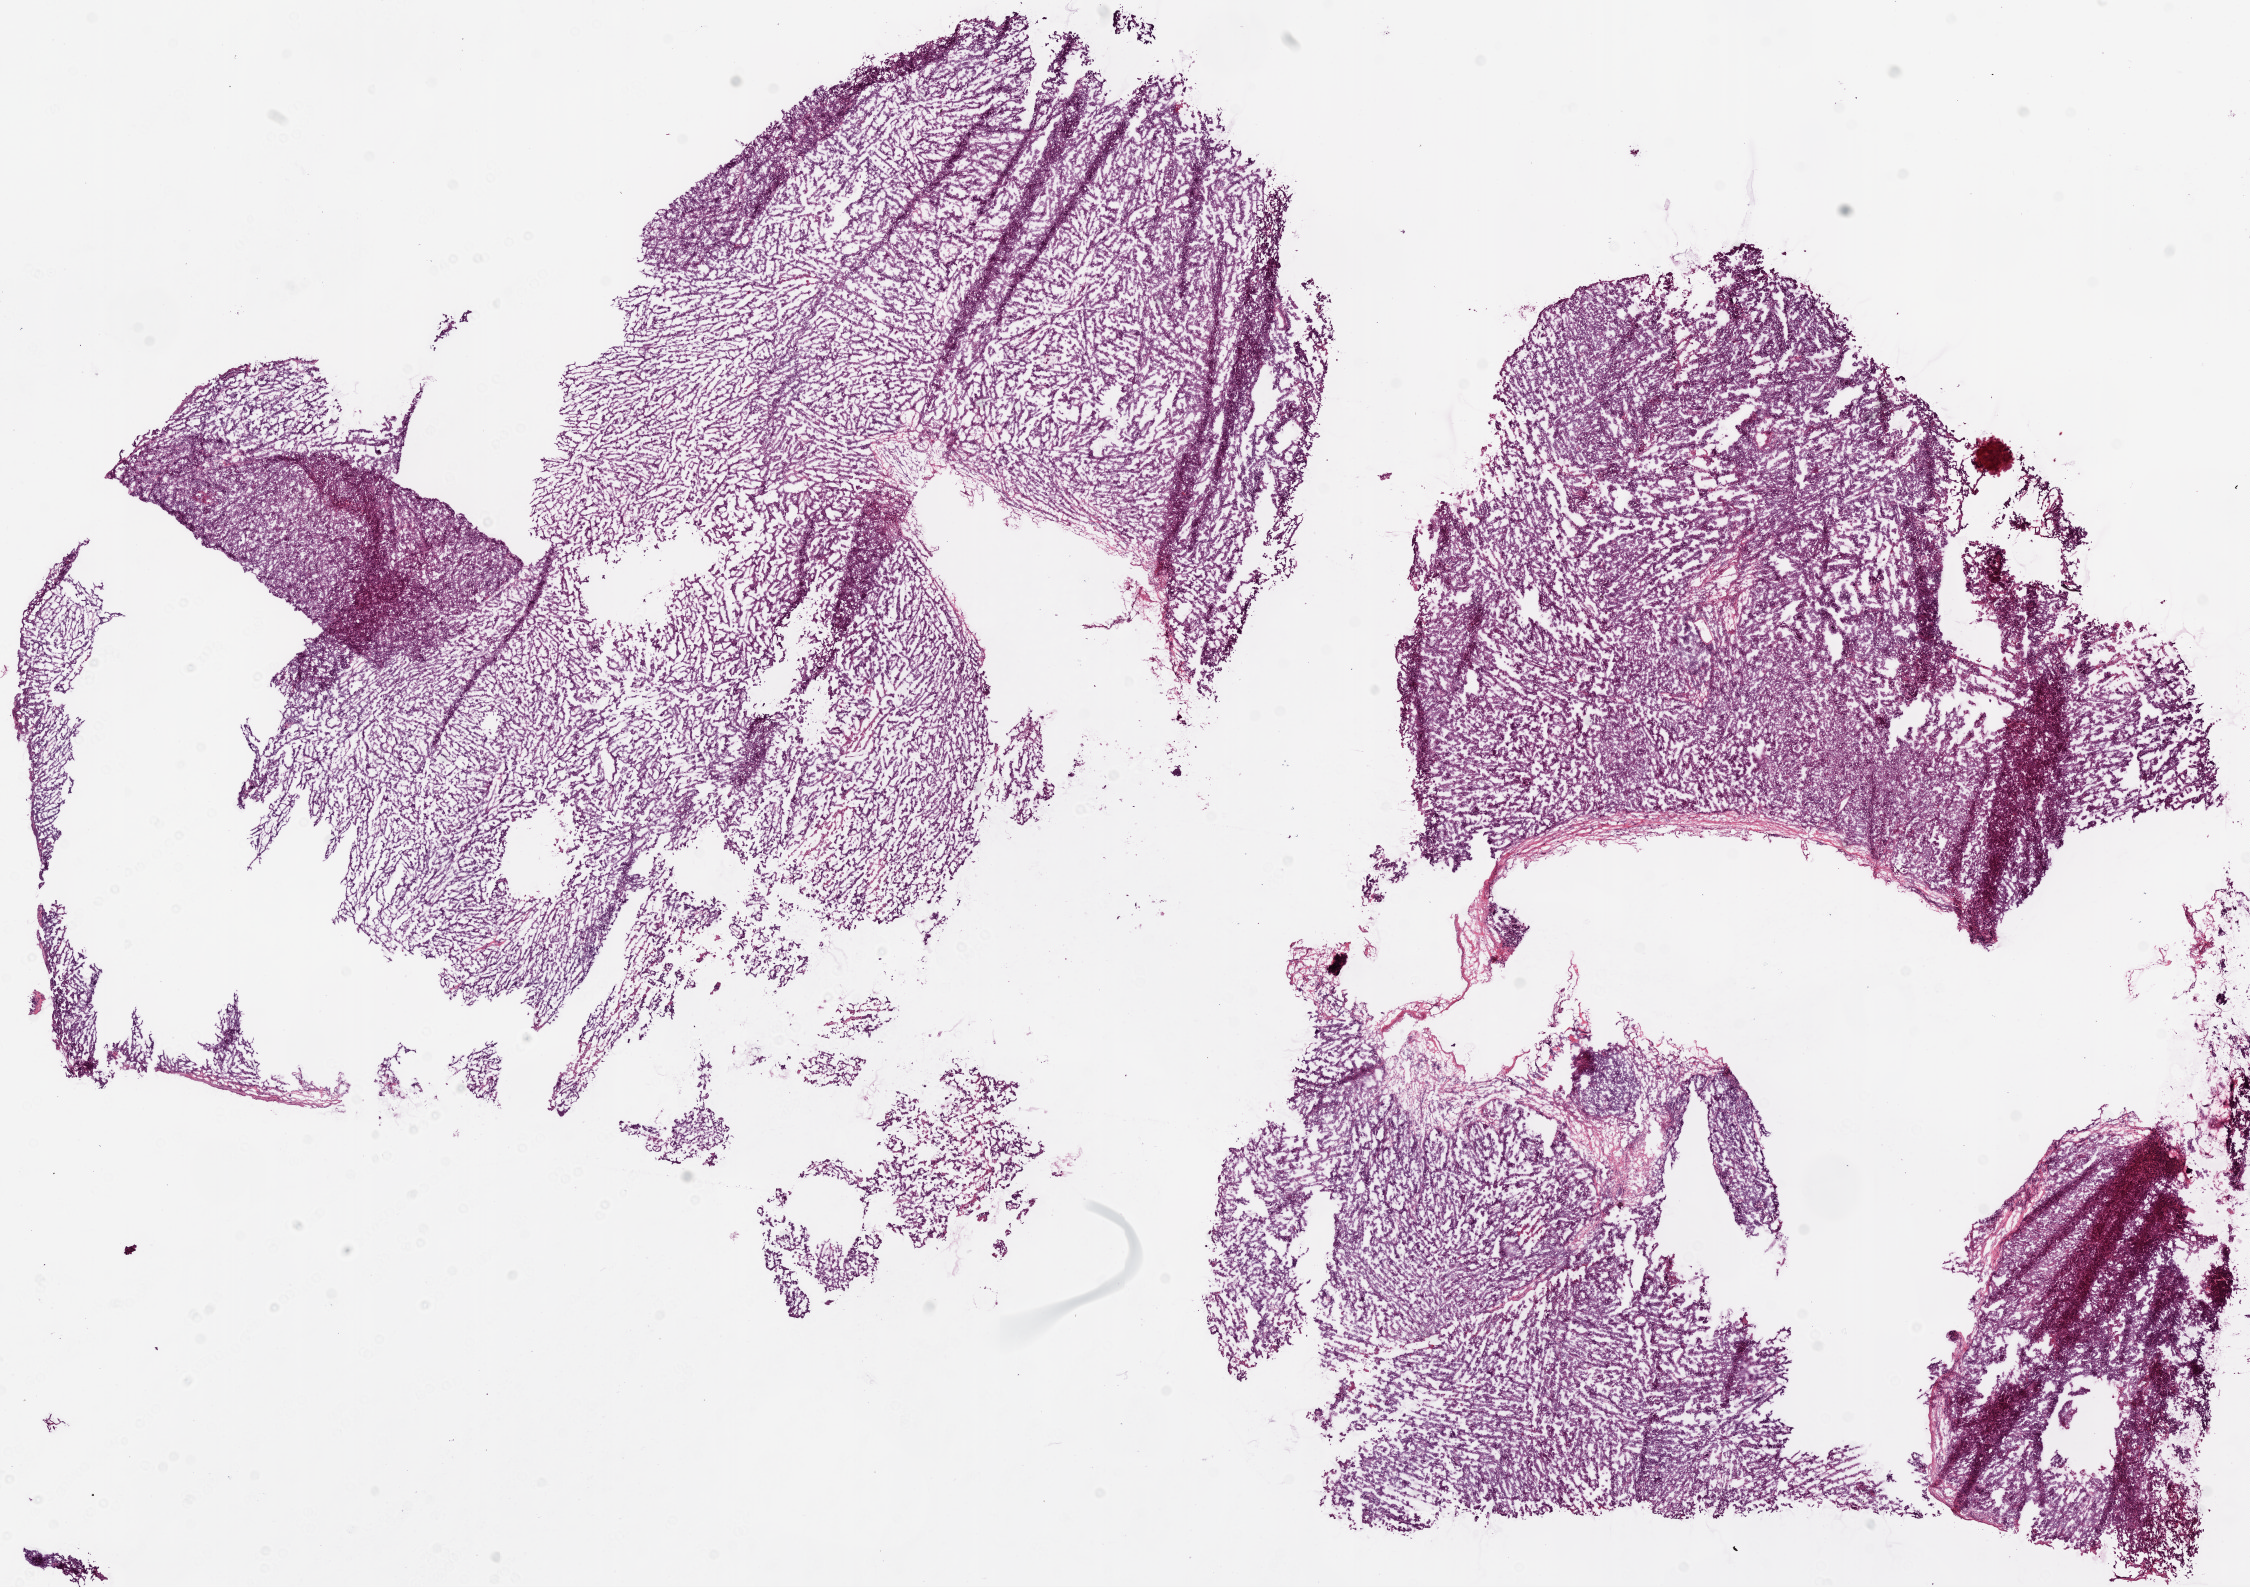
H&E whole-slide image, whole scanned area (about 18.1 x 12.7 mm, from a 20x scan) shown as a low-resolution overview, frozen section from the bottom of the tissue portion, ovary, primary tumour sample. Female patient; age at initial diagnosis 65 years. Histologic grade: G3 (poorly differentiated). Composition of this section per pathologist review: tumour cells 94%, tumour nuclei 99%, normal cells 0%, stromal cells 1%, necrosis 5%.
Pathologic diagnosis: Serous cystadenocarcinoma, NOS. FIGO stage: IIIC. Laterality: bilateral.